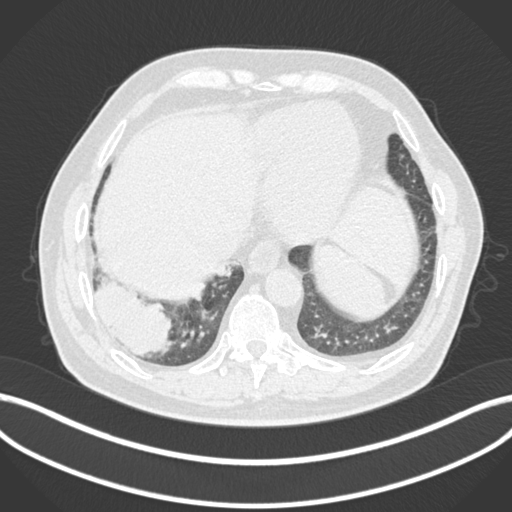
Chest CT, one axial slice. Position 27 of 200 along the scan axis. 120 kVp. Lung window (W 1500 / L -600 HU). 512 × 512 image matrix, field of view 400 × 400 mm. Male patient, age 59 years.
Annotated regions visible in this slice (bounding box drawn by a radiologist):
- lung tumour (recorded histology: adenocarcinoma): bounding box [x1, y1, x2, y2] px = [86, 271, 173, 359]